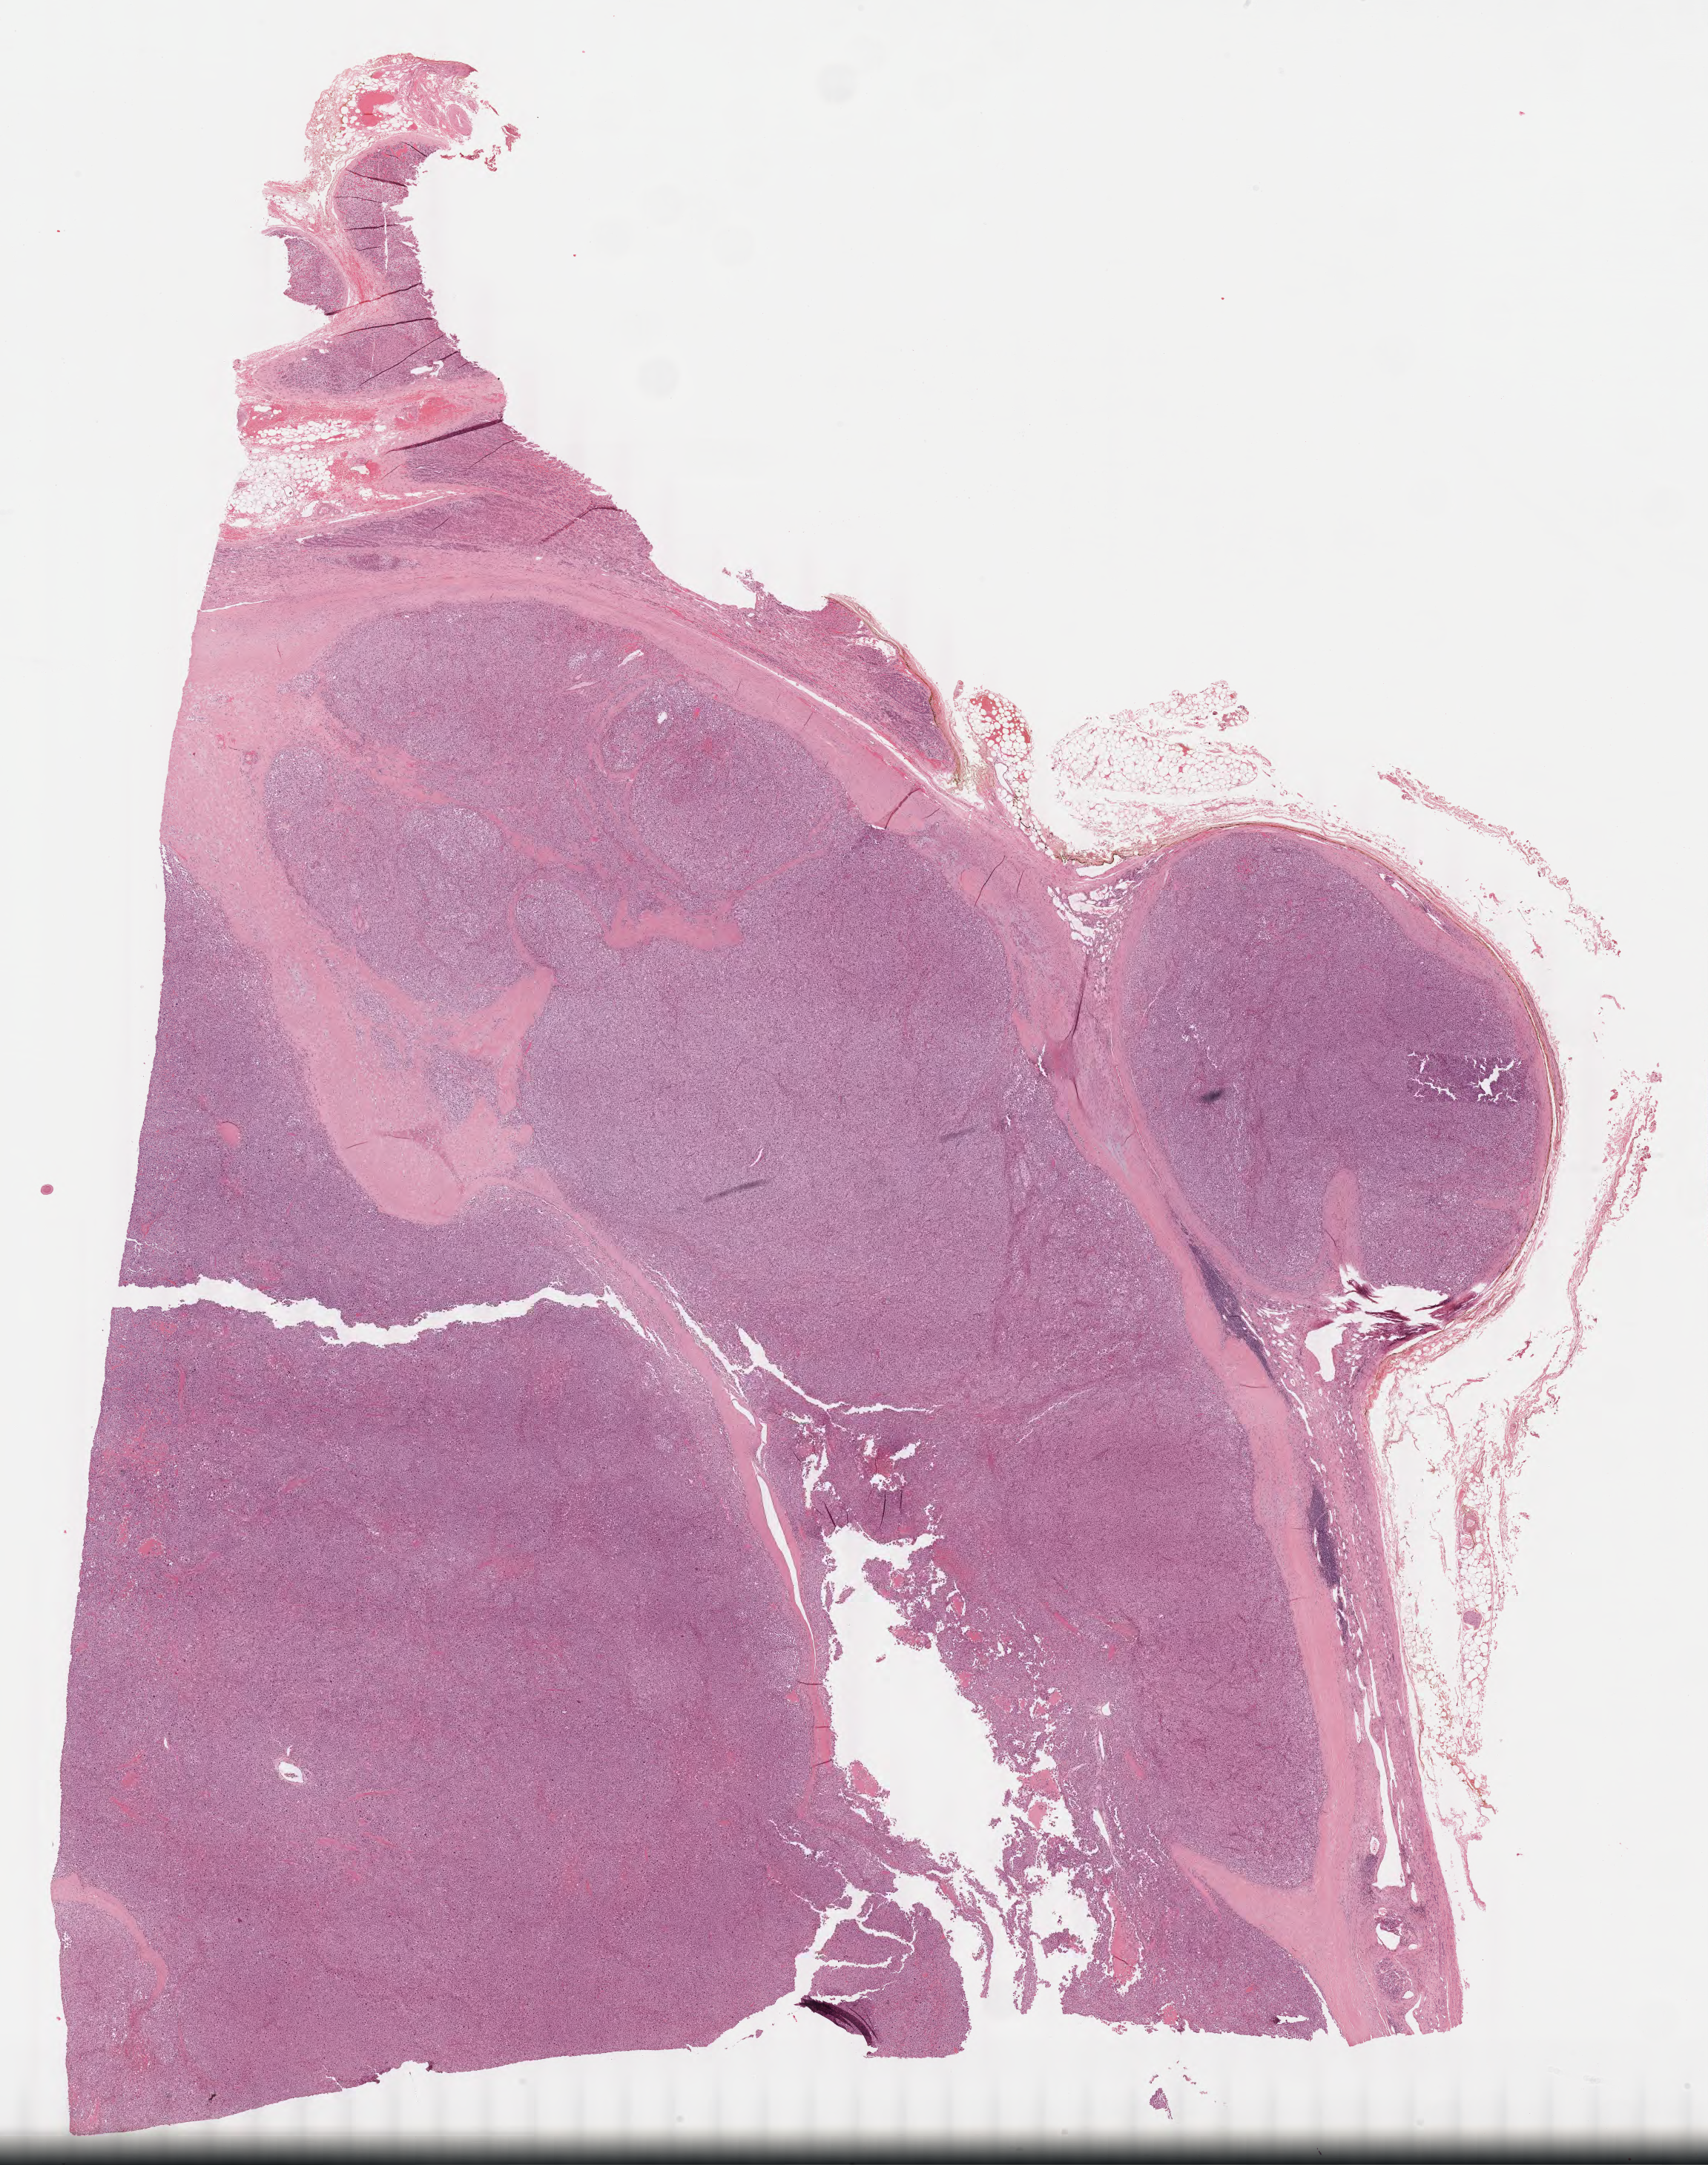
Digitized Hematoxylin and eosin (H&E) stained tissue section (whole slide), whole scanned area (about 18.2 x 23.1 mm, slide scanned at 40x) shown as a low-resolution overview. Formalin-fixed paraffin-embedded (FFPE) diagnostic section. Sample: primary tumour, adrenal cortex. Male, age 63 years at initial diagnosis.
Laterality: left. Histologic diagnosis: Adrenal cortical carcinoma (cortex of adrenal gland).